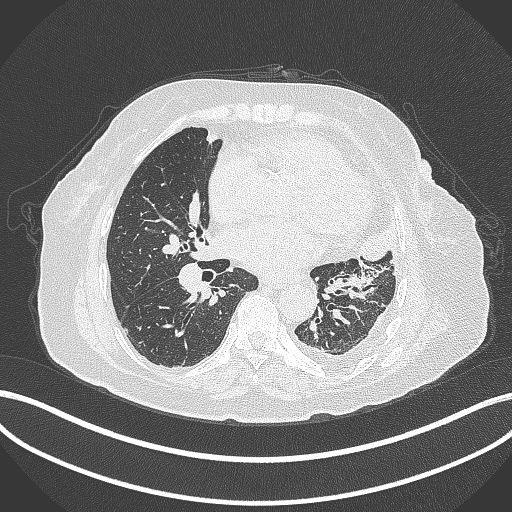
Chest CT, one axial slice. Slice 169 of 399 in the series (ordered by position). Reconstruction kernel B70f. 120 kVp. Lung window (W 1500 / L -600 HU). 1 mm slice thickness. 512 × 512 image matrix. Female patient, age 75 years. From the clinical record (not read from this slice): clinical TNM (as recorded): T3 N3 M1.
Outlined on this slice (bounding box drawn by a radiologist):
- lung tumour (recorded histology: adenocarcinoma): bounding box [x1, y1, x2, y2] px = [356, 222, 404, 265]